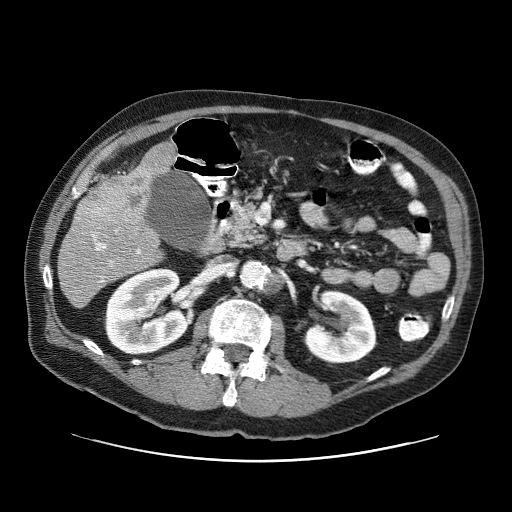
Contrast-enhanced abdominal CT (liver protocol), one axial slice. Slice 24 of 87 in the series (ordered by position). Reconstruction kernel STANDARD. One of 3 acquisitions stored at this slice position. Soft-tissue window (W 400 / L 40 HU). 2.5 mm slice thickness. 512 × 512 image matrix, field of view 400 × 400 mm. From the clinical record (not read from this slice): diagnosis: hepatocellular carcinoma (patient treated with transarterial chemoembolisation; whether this scan precedes or follows treatment is not stated here); TNM stage (as recorded): Stage-IIIA; Child-Pugh class: A; tumour differentiation: well differentiated; tumour nodularity: multinodular.
Annotated regions visible in this slice (semi-automatic segmentation, software-assisted and operator-edited):
- liver parenchyma outside the tumour (the mass and vessels are separate outlines, so this box may not span the whole liver): bounding box [x1, y1, x2, y2] px = [58, 142, 176, 308]
- mass: [75, 163, 156, 232]
- liver vessels: [93, 231, 141, 282]